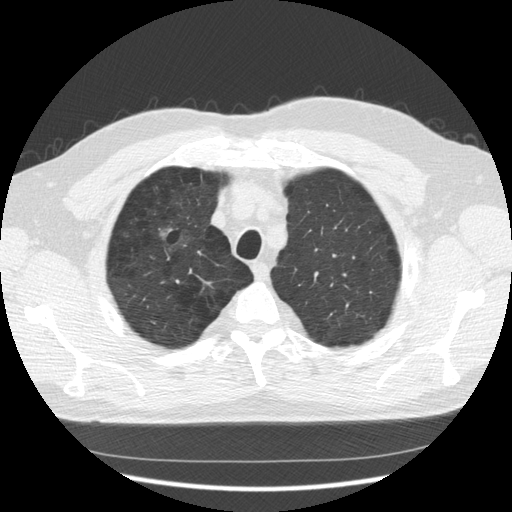
Low-dose screening chest CT, one axial slice; position 103 of 133 along the scan axis; reconstruction kernel STANDARD; lung window (W 1500 / L -600 HU); 2.5 mm slice thickness; 512 × 512 image matrix, field of view 369 × 369 mm.
Outlined on this slice (manually delineated by an expert):
- lesion 1 (tumor, upper lobe of right lung): box from (x=160, y=228) to (x=172, y=238) px